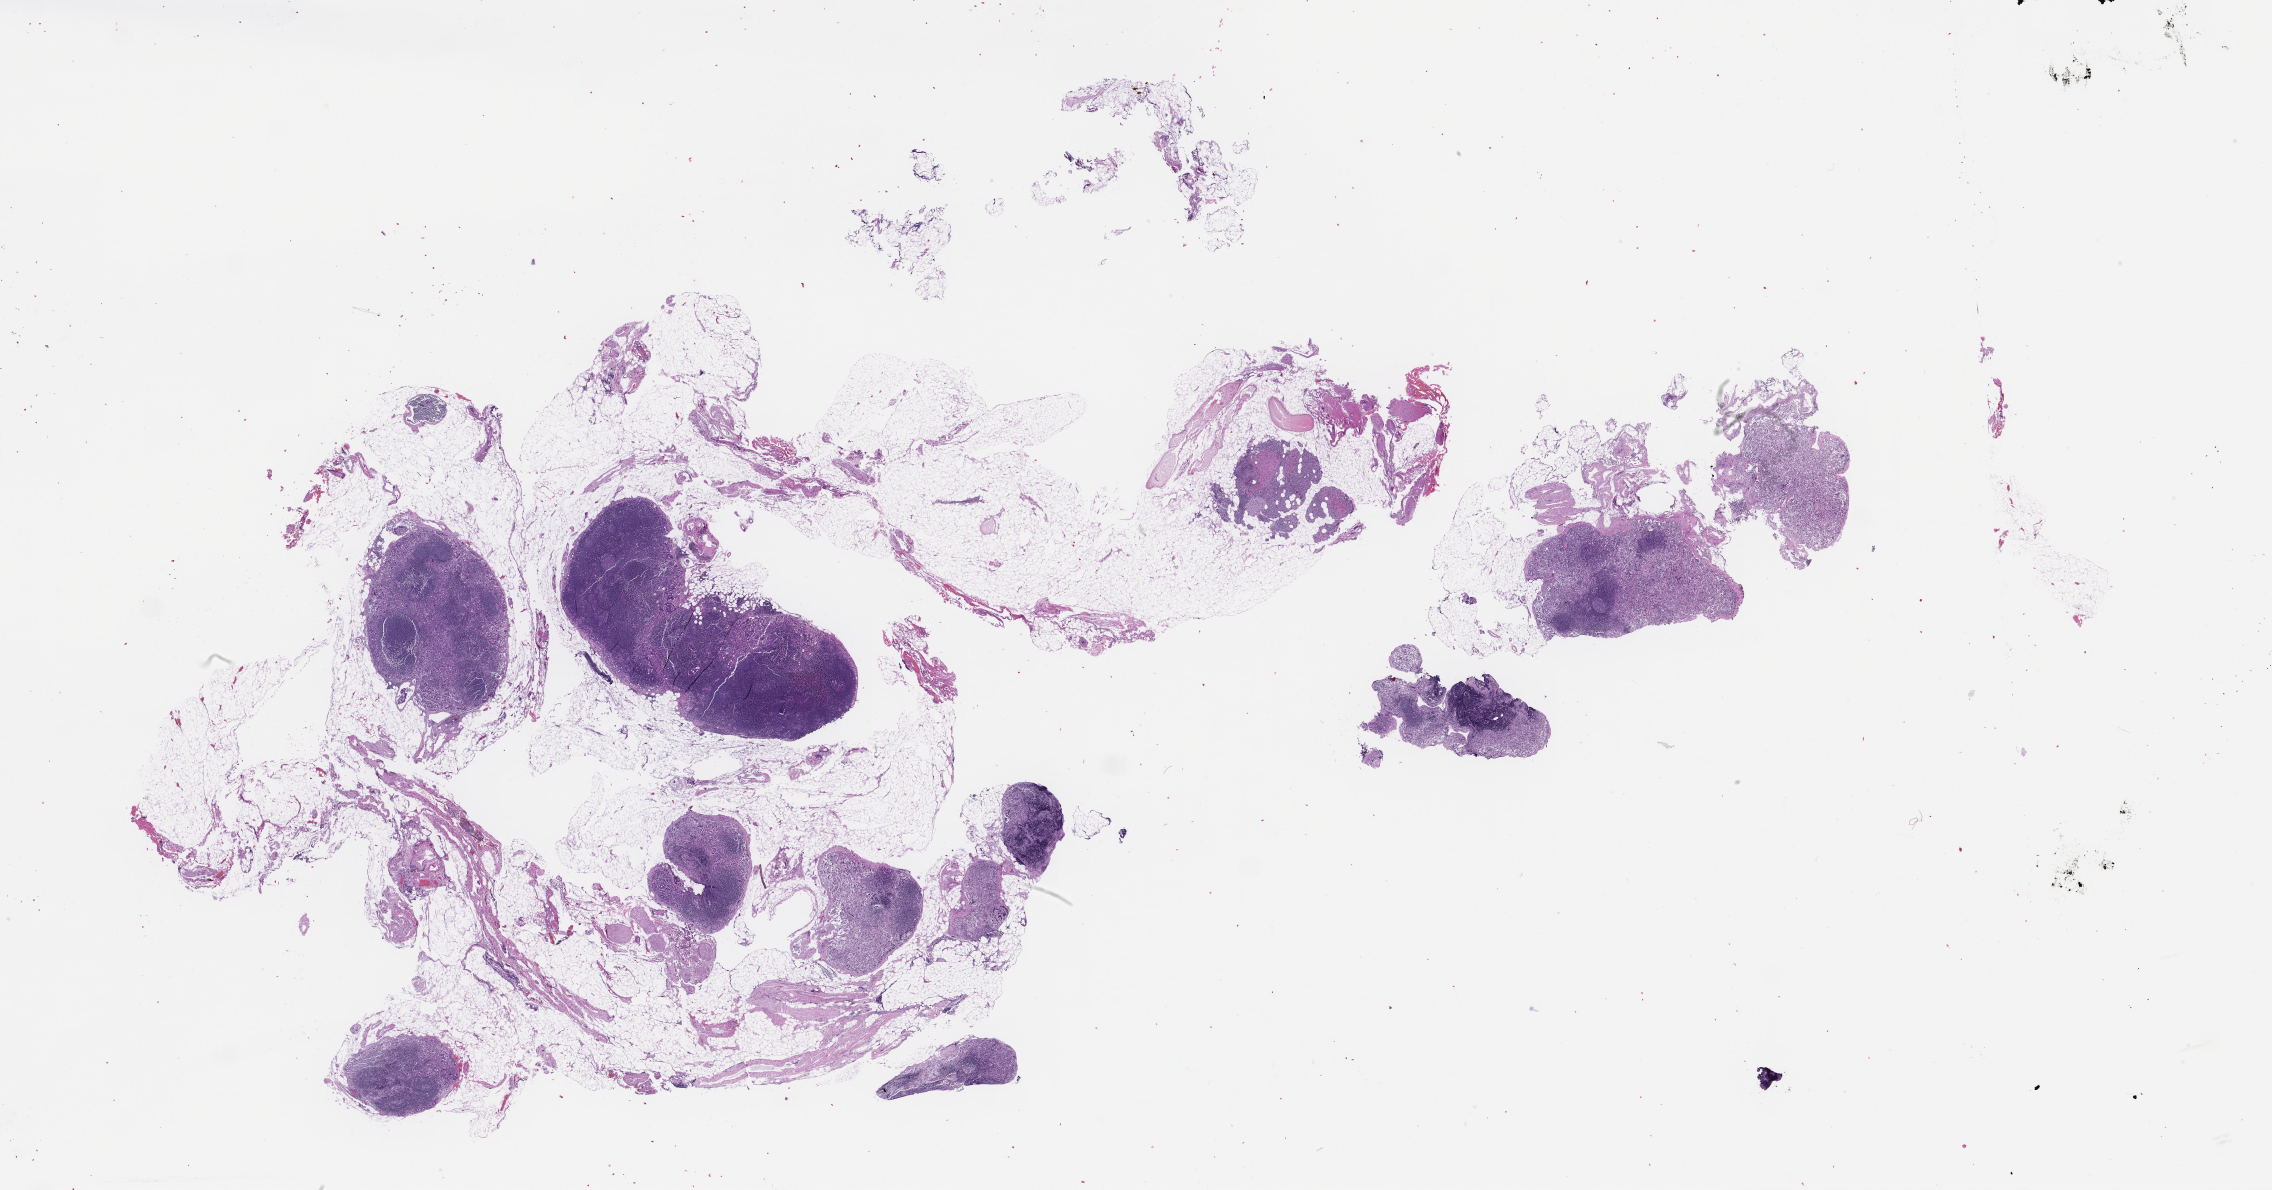
Hematoxylin and eosin (H&E) whole-slide image — shown as a low-resolution overview of the whole scanned area (about 36.7 x 19.2 mm); formalin-fixed paraffin-embedded section. Patient: female.
This section: metastatic tumor tissue. Primary diagnosis of the patient: Adenocarcinoma of the Gastroesophageal Junction.